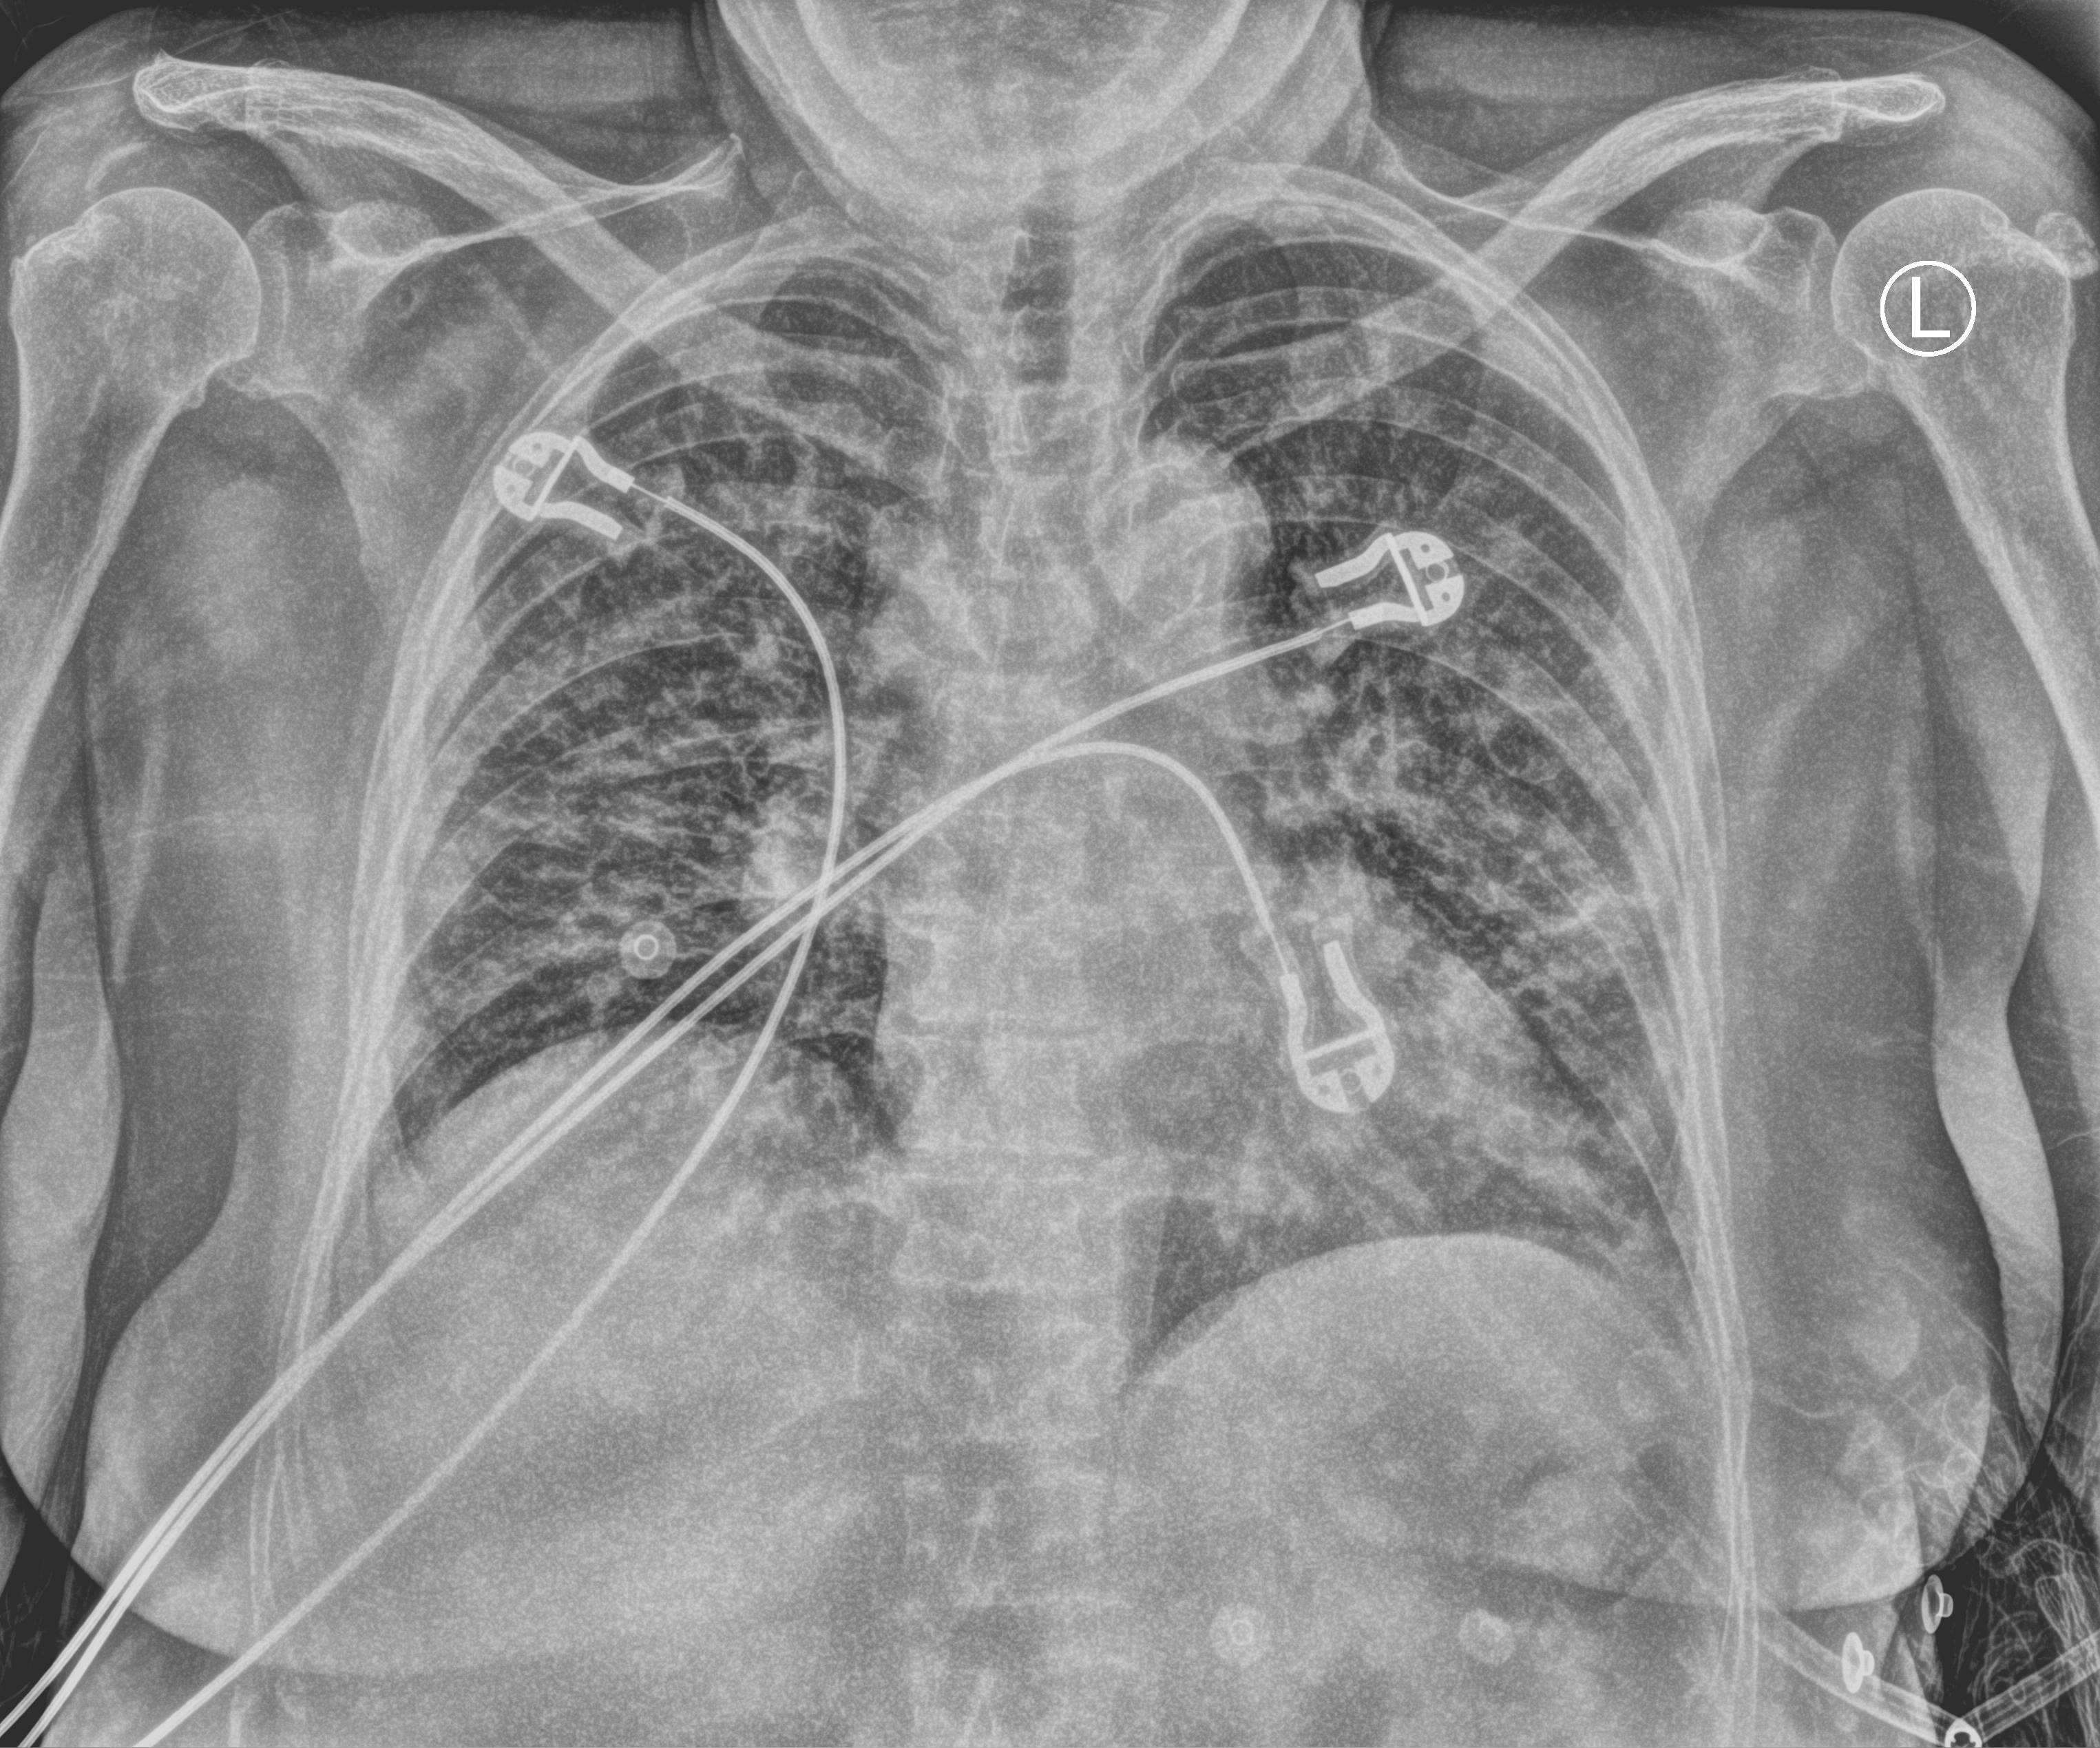
Bedside chest radiograph (computed radiography); anteroposterior (AP) projection. Patient hospitalised with COVID-19; female, aged 75–90 years.
Admission-level facts for this patient (not findings on this image; timing relative to this image not recorded):
- admitted to intensive care during this hospital stay: no
- mechanically ventilated during this hospital stay: no